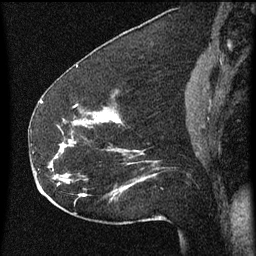
Breast MRI (dynamic contrast-enhanced), one sagittal slice; position 28 of 60 along the scan axis; dynamic contrast-enhanced series, image 2 of 3 at this slice position (ordered by acquisition); 1.5 T; TE 4.2 ms, TR 8 ms; 2 mm slice thickness; 256 × 256 image matrix. Patient: female, 52 years.
Outlined on this slice (semi-automatically segmented with operator editing):
- analysis volume of interest (the breast-tissue region the enhancement analysis was run in; not a lesion): bounding box <54,110,160,207> (left, top, right, bottom; pixels)
- tumour enhancement mask (voxels above the 70 % enhancement threshold inside the analysis volume of interest): <62,112,95,197>